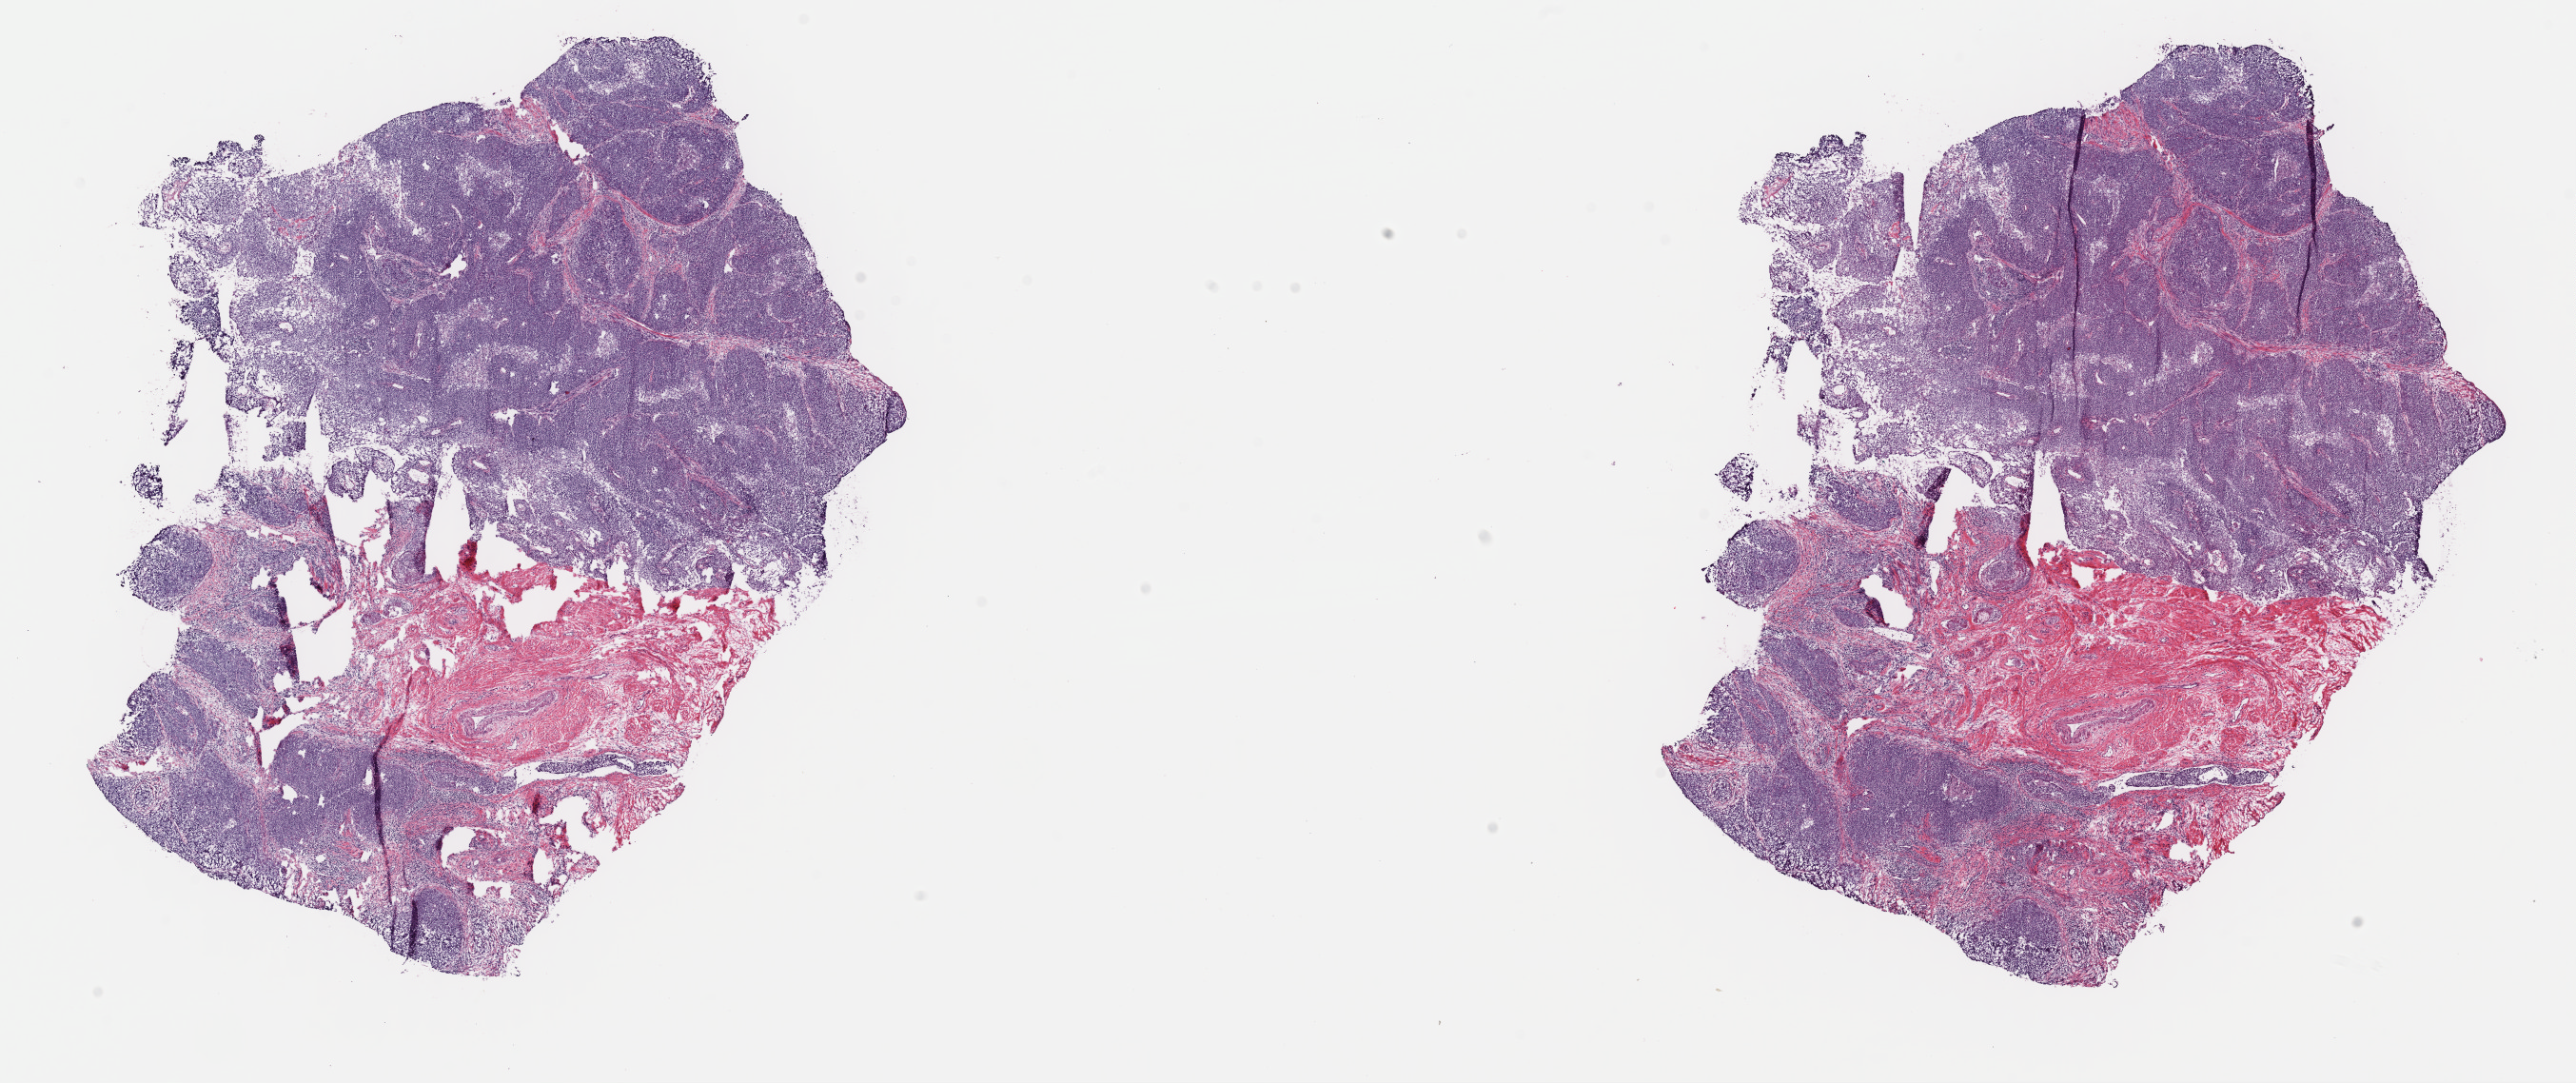
Digitized H&E-stained tissue section (whole slide) — shown as a low-resolution overview of the whole scanned area (about 21.4 x 9.0 mm, acquisition: 40x scan). Frozen section from the top of the tissue portion. Cervix, primary tumour sample. Patient: female, age at initial diagnosis 51 years. Histologic grade: G3 (poorly differentiated). Composition of this section per pathologist review: tumour cells 70%, tumour nuclei 70%, normal cells 0%, stromal cells 25%, necrosis 5%. Infiltration values recorded for this section: lymphocyte infiltration 60%, monocyte infiltration 10%, neutrophil infiltration 10%.
Diagnosis: Adenocarcinoma, NOS (cervix uteri). Lymph nodes positive (case pathology): 2 of 28 examined. FIGO stage: IIIB.